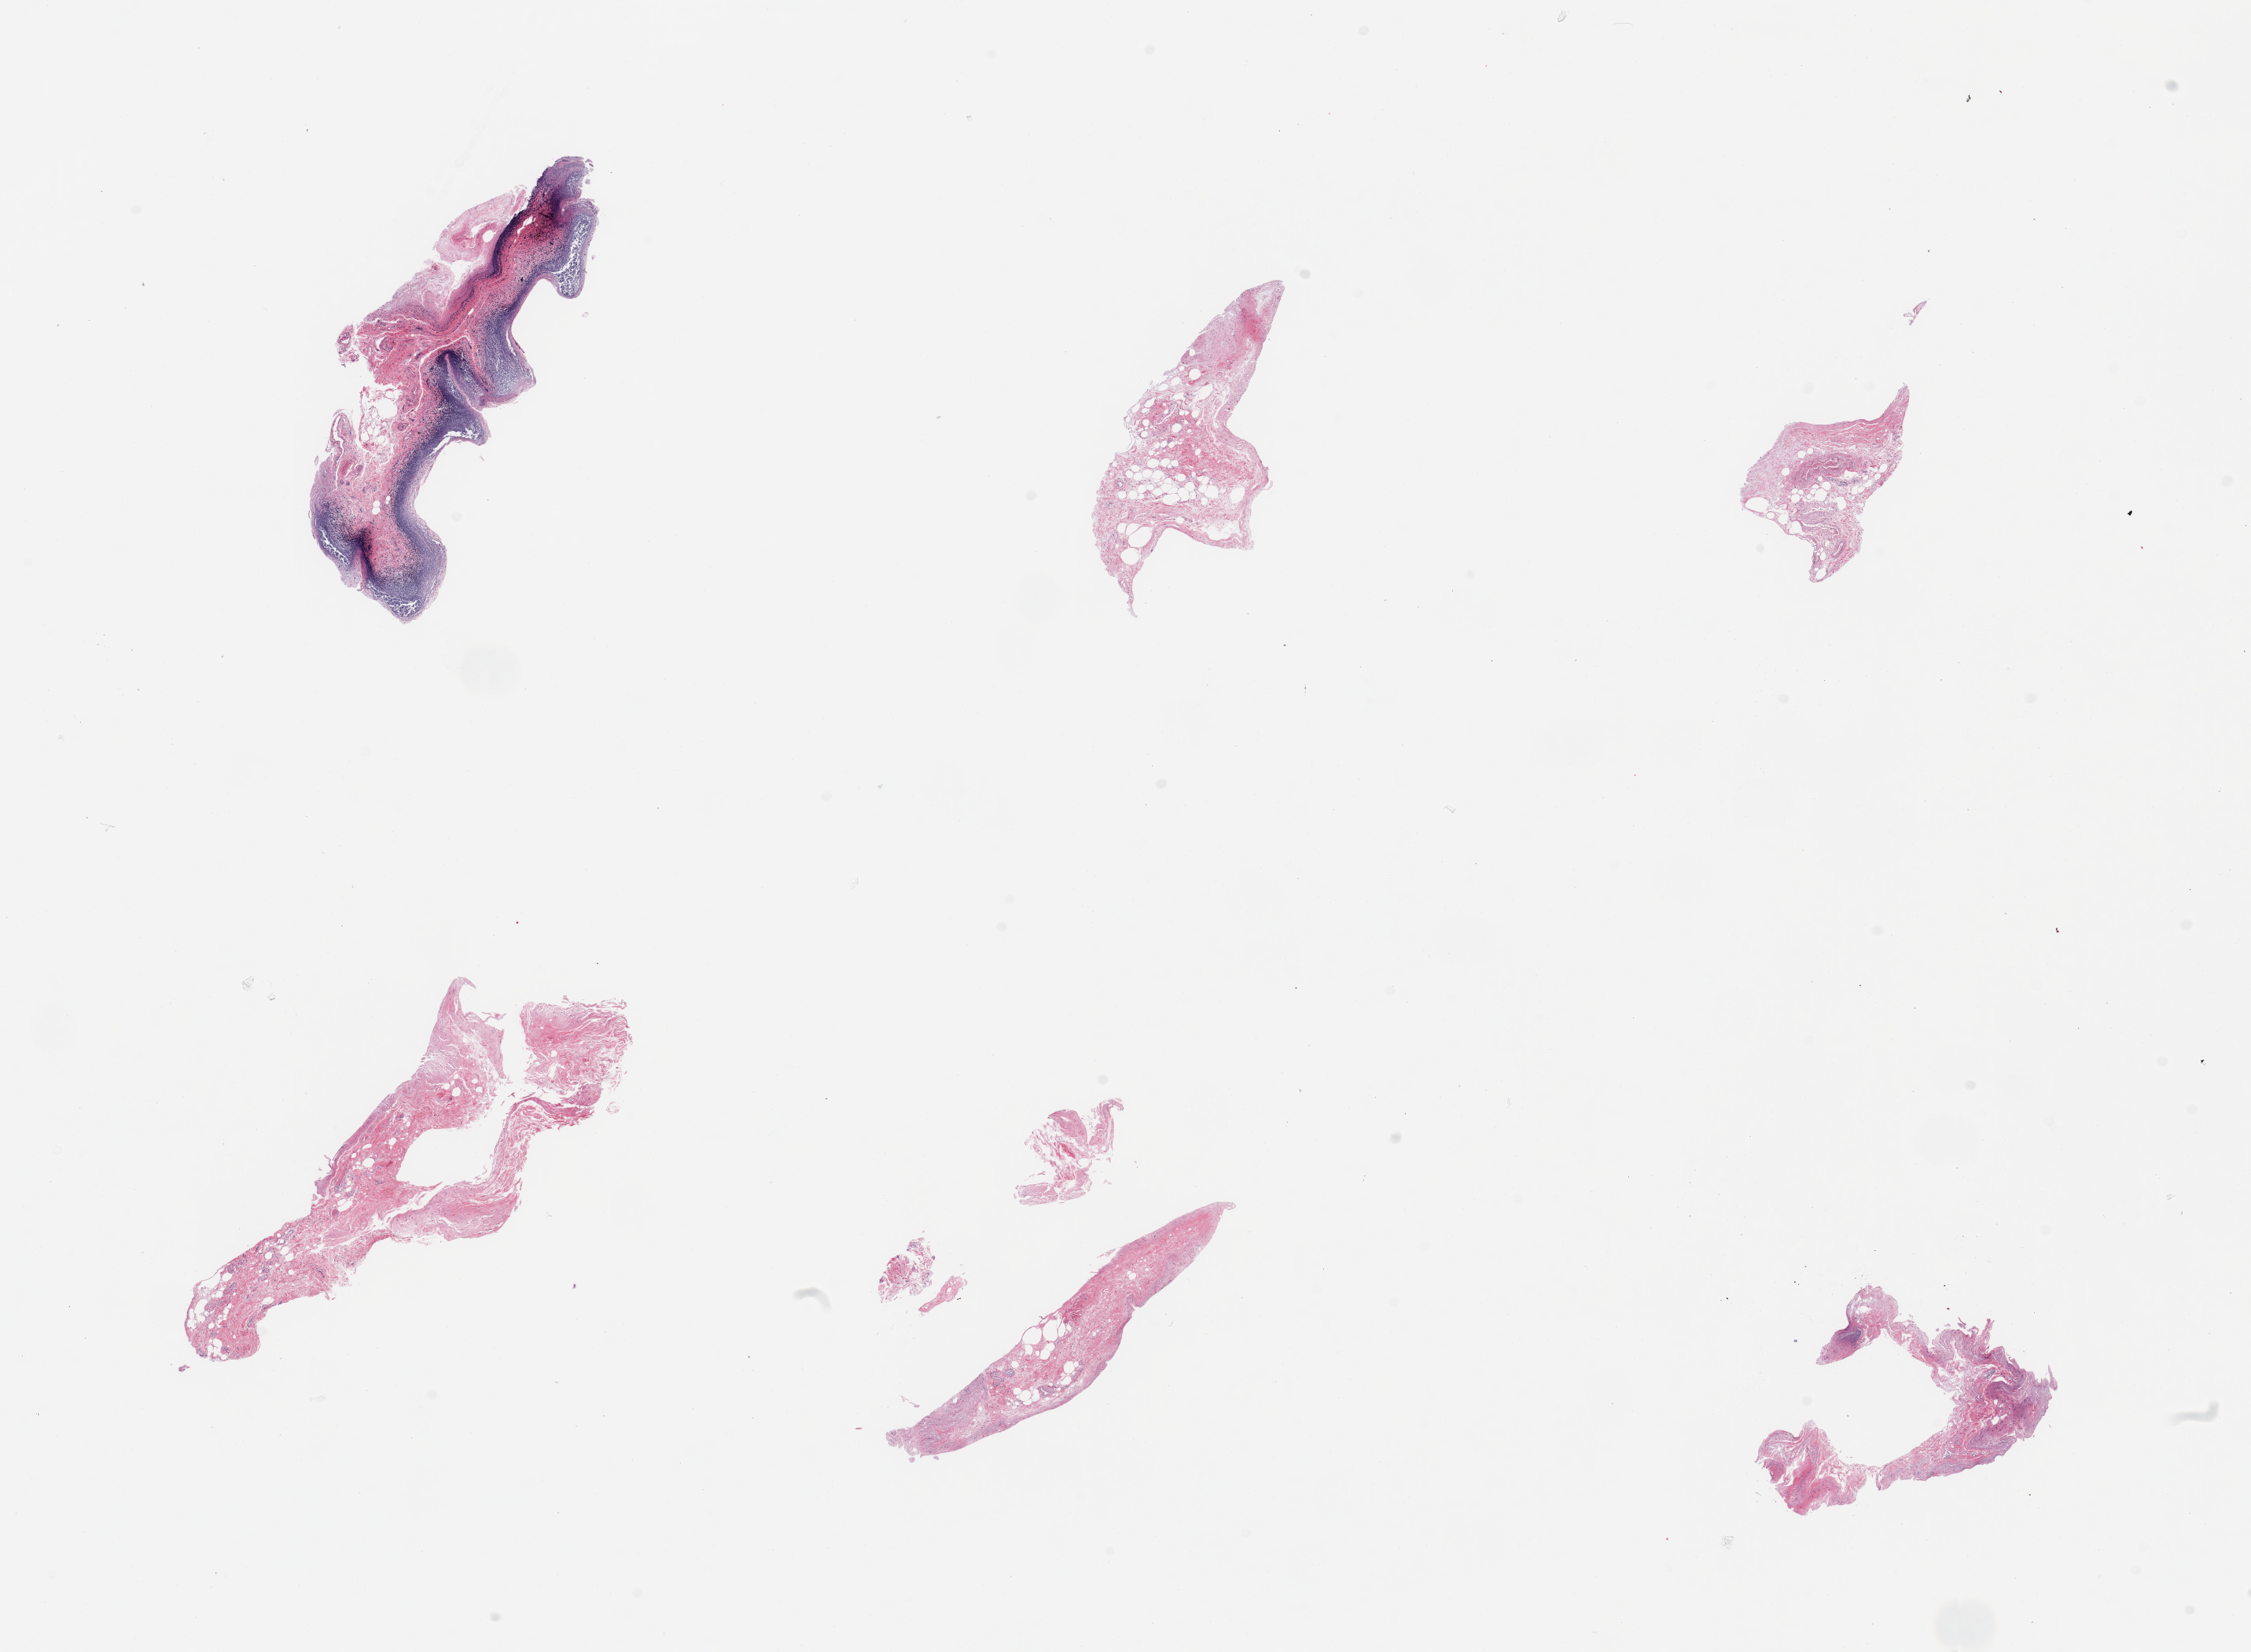
Whole-slide image, haematoxylin and eosin stain — shown as a low-resolution overview of the whole scanned area (about 22.6 x 16.6 mm, from a 20x scan); PAXgene-fixed paraffin-embedded (PFPE) section; section of ileum (target tissue); tissue donor sample. Donor: female.
• reviewer comment on this tissue sample: 6 pieces, only with trace residual lymphoid elements